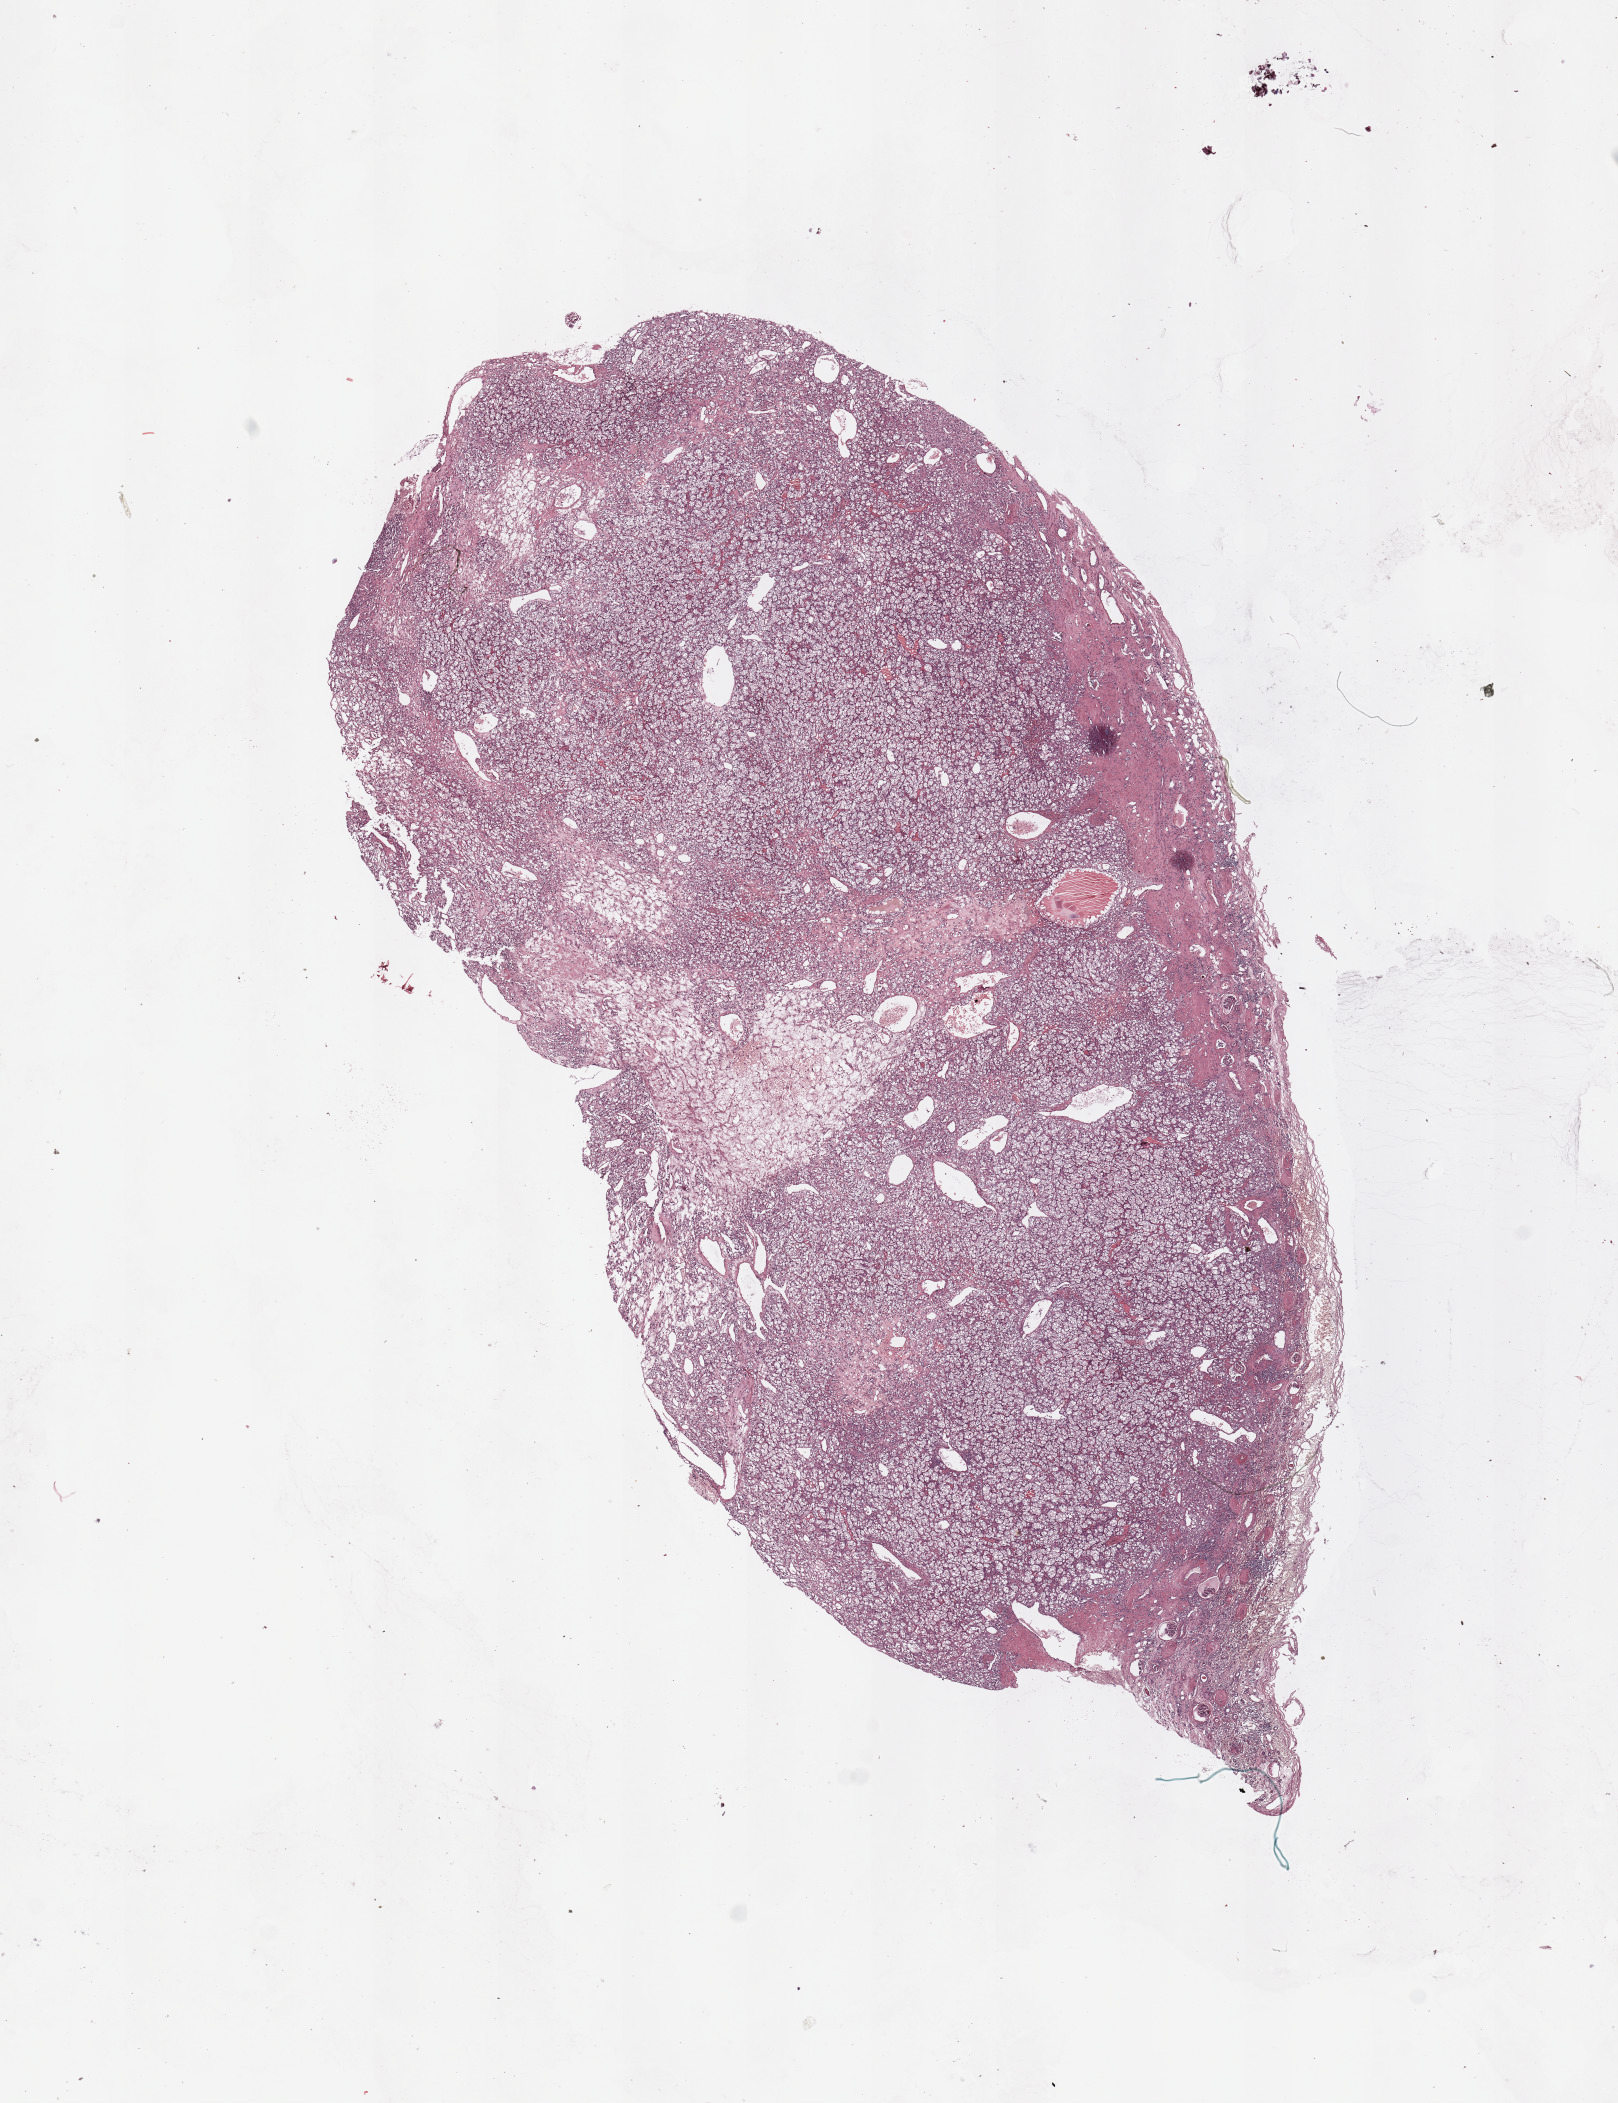
Digitized Hematoxylin and eosin (H&E) stained tissue section (whole slide) — whole scanned area (about 12.8 x 16.6 mm) shown as a low-resolution overview. Tumour tissue sample, kidney. 68-year-old male patient. Histologic grade: G1 (well differentiated).
* diagnosis: Renal cell carcinoma, NOS
* AJCC pathologic stage: III
* primary tumour site (as recorded): upper pole